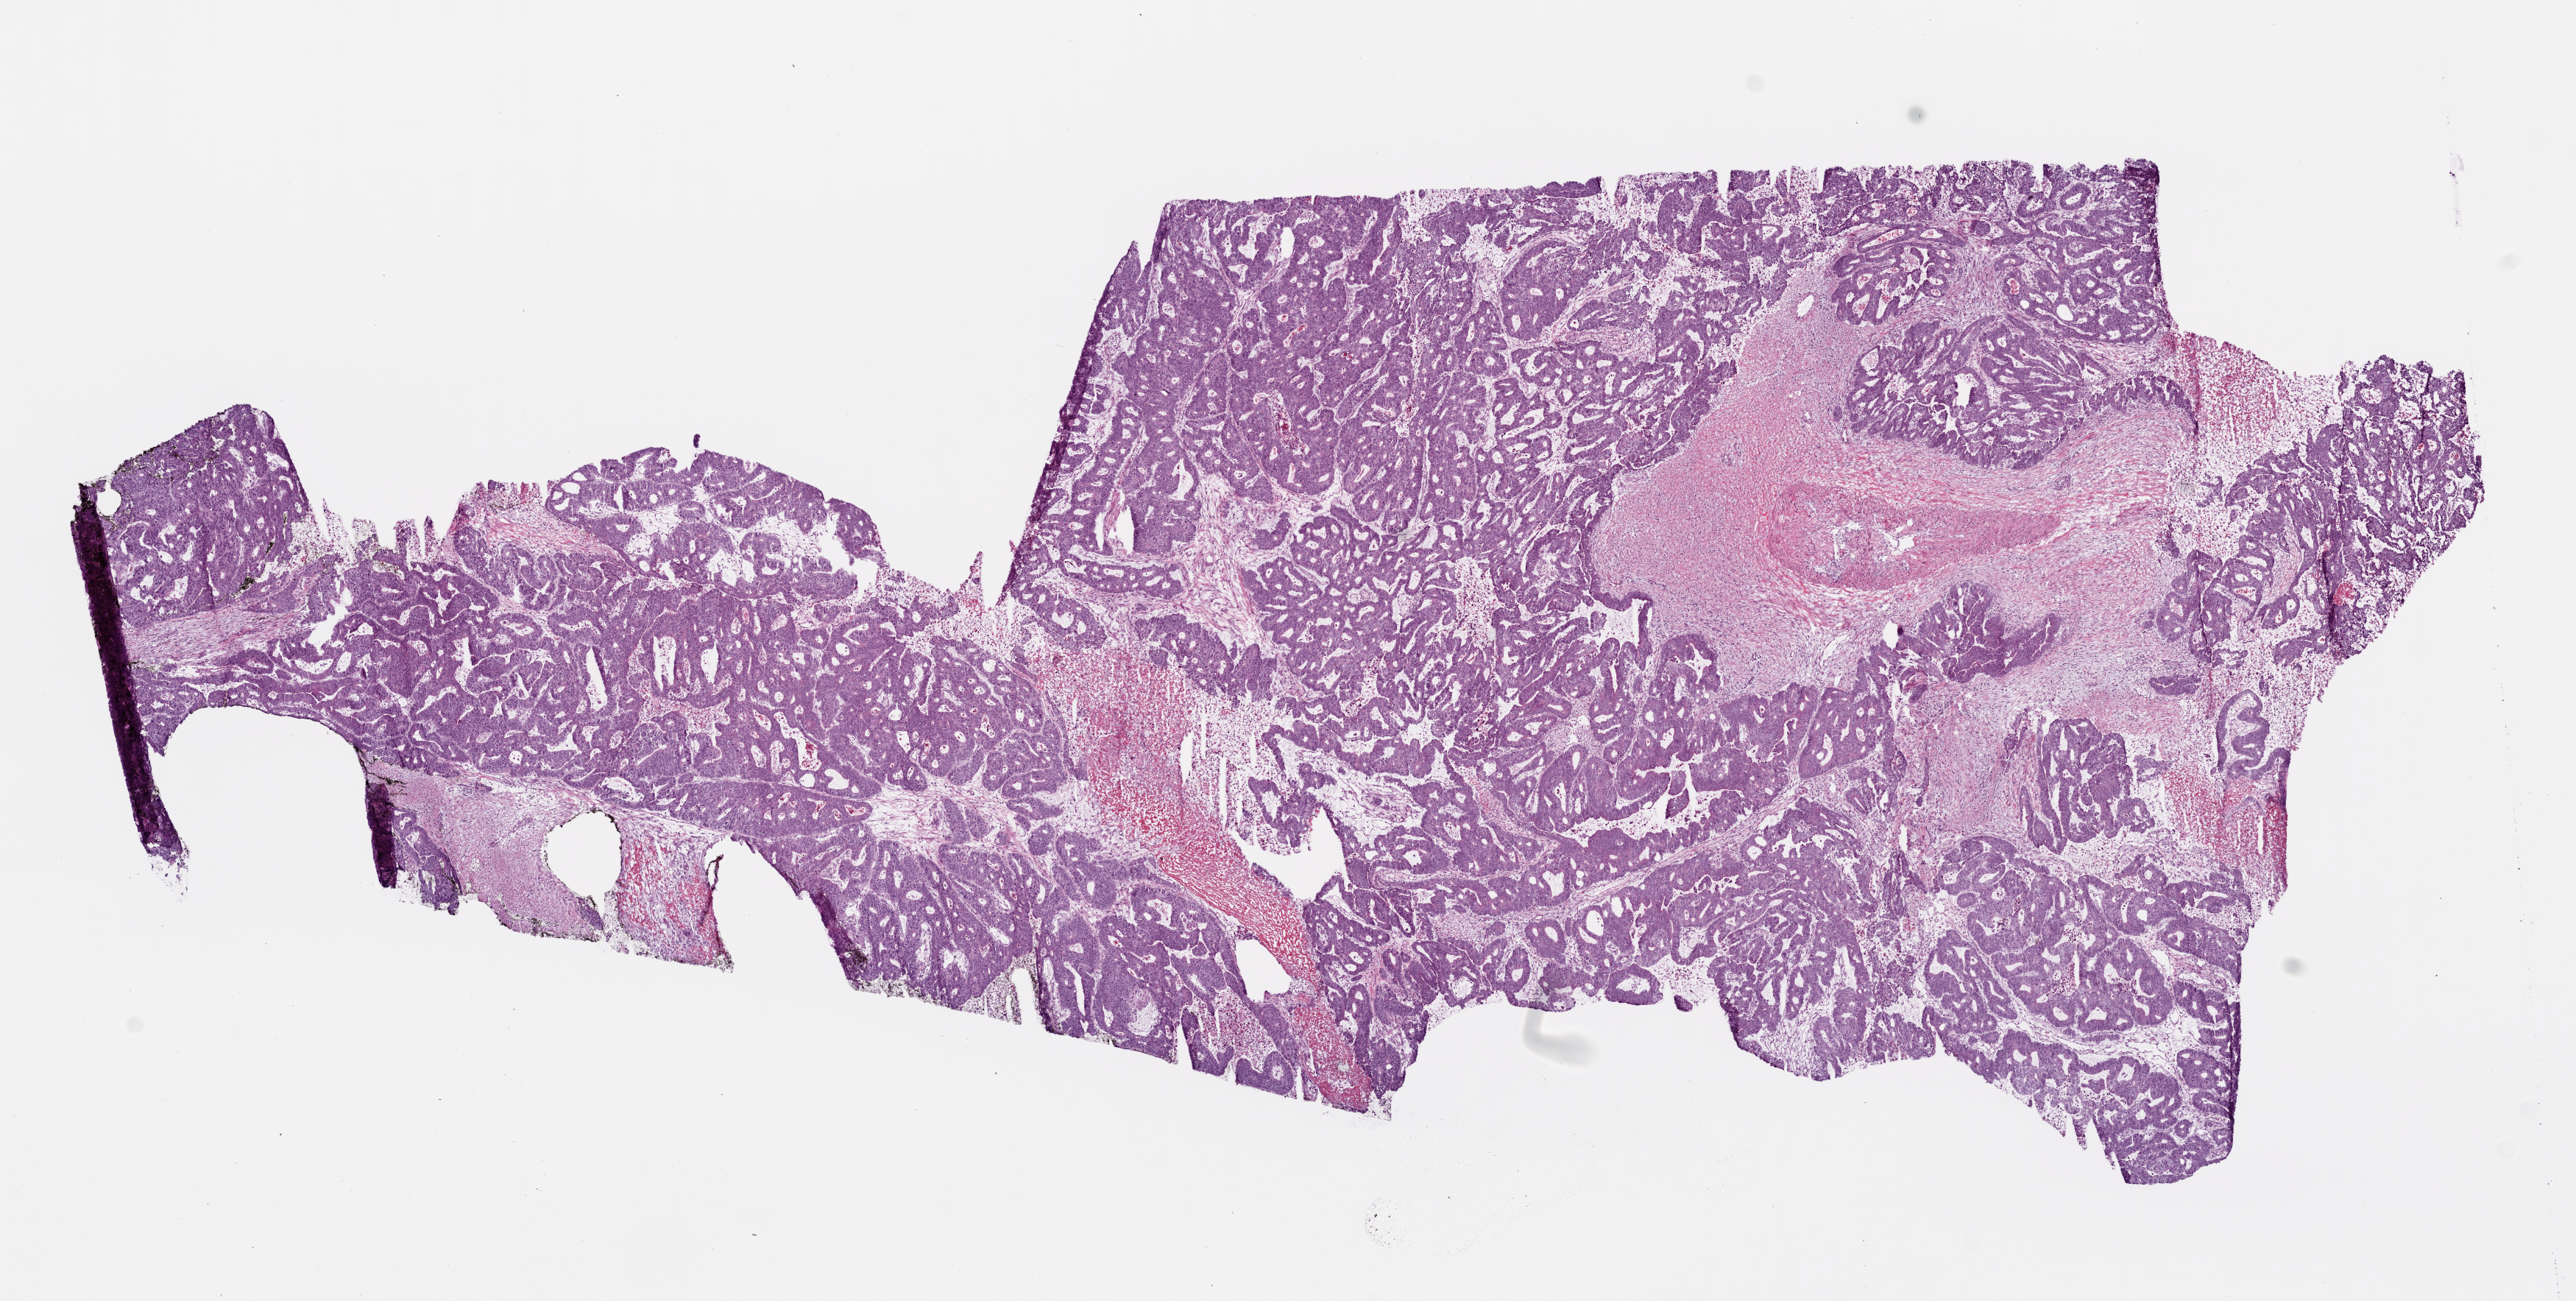
Whole-slide histology image, Hematoxylin and eosin (H&E) stained — a low-resolution overview of the entire scanned area, about 14.0 x 7.1 mm (slide scanned at 20x), frozen section, sample: primary tumour, colon. Patient: male, age at initial diagnosis 78 years. Slide review estimates, as recorded: tumour cells 90%, tumour nuclei 80%, normal cells 0%, stromal cells 0%, necrosis 10%. Inflammatory infiltration, as recorded: lymphocyte infiltration 5%, monocyte infiltration 1%, neutrophil infiltration 2%.
TNM: T4b N0 M0. AJCC pathologic stage: IIC. Lymph nodes positive (case pathology): 0 of 30 examined. Histologic diagnosis: Adenocarcinoma, NOS.